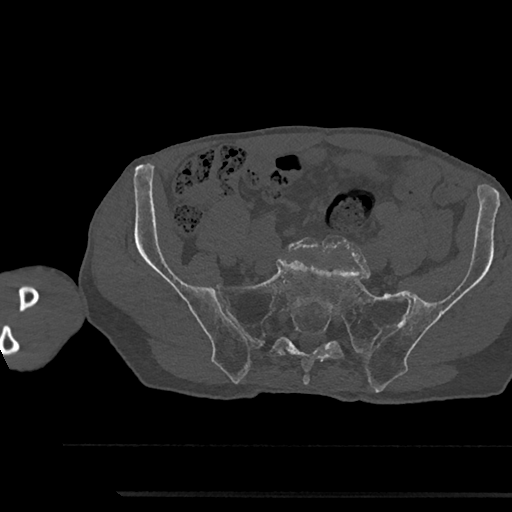
CT including the spine, one axial slice. Slice 281 of 797 in the series (ordered by position). Reconstruction kernel Br40s/3. 120 kVp. Bone window (W 1800 / L 400 HU). 0.5 mm slice thickness. 512 × 512 image matrix, field of view 367 × 367 mm. Patient: male, 79 years. Case-level facts recorded for this patient, not image findings: primary cancer: prostate.
Structures marked on this image (semi-automatically segmented with operator editing):
- L5 vertebra: bounding box (x1, y1, x2, y2) in pixels: (288, 237, 318, 251)